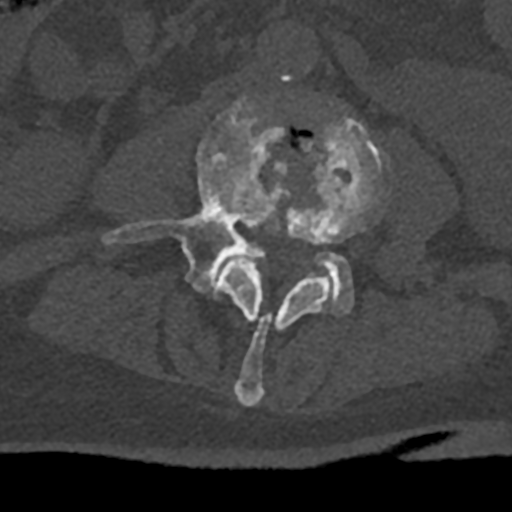
CT including the spine, one axial slice. Slice 288 of 797 in the series (ordered by position). 120 kVp. Bone window (W 1800 / L 400 HU). 512 × 512 image matrix, field of view 160 × 160 mm. Male patient, age 74 years. From the clinical record (not read from this slice): primary cancer: renal.
Outlined on this slice (semi-automatically segmented with operator editing):
- L3 vertebra: bounding box <217,116,390,406> (left, top, right, bottom; pixels)
- L4 vertebra: <103,100,354,315>